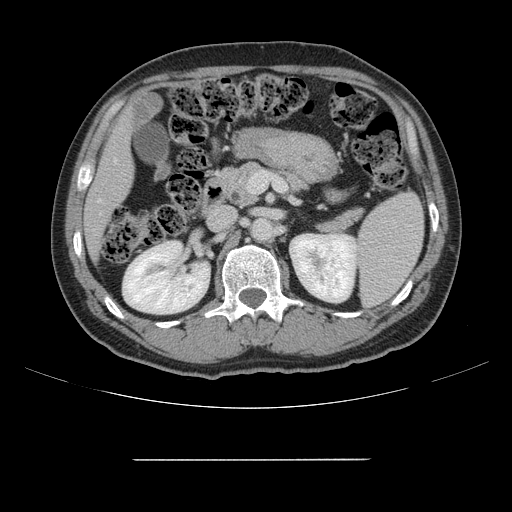
Contrast-enhanced abdominal CT, one axial slice; position 69 of 164 along the scan axis; 120 kVp; intravenous contrast given; soft-tissue window (W 400 / L 40 HU); 2.5 mm slice thickness; 512 × 512 image matrix, field of view 404 × 404 mm. Male patient, age 54 years. From the clinical record (not read from this slice): diagnosis: colorectal cancer liver metastases, imaged before liver resection; multiple liver metastases: yes; largest metastasis: 1 cm; disease in both lobes: no.
Structures marked on this image (expert manual segmentation):
- hepatic veins: bounding box [x1, y1, x2, y2] px = [98, 160, 116, 202]
- liver: [85, 116, 133, 256]
- planned liver remnant (the part of the liver to remain after resection): [85, 115, 133, 256]